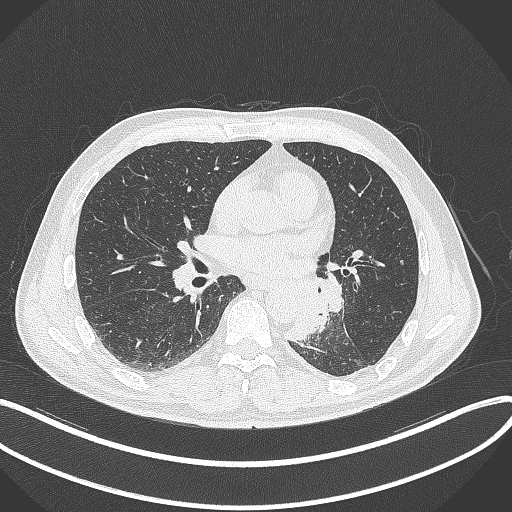
Chest CT, one axial slice. Position 160 of 329 along the scan axis. Reconstruction kernel B70f. 120 kVp. Lung window (W 1500 / L -600 HU). 1 mm slice thickness. 512 × 512 image matrix, field of view 400 × 400 mm. Male patient, age 59 years. Case-level facts recorded for this patient, not image findings: clinical TNM (as recorded): T2a N2 M0.
Outlined on this slice (rectangle marked by the reading radiologist):
- lung tumour (recorded histology: squamous cell carcinoma): box from (x=285, y=287) to (x=328, y=342) px